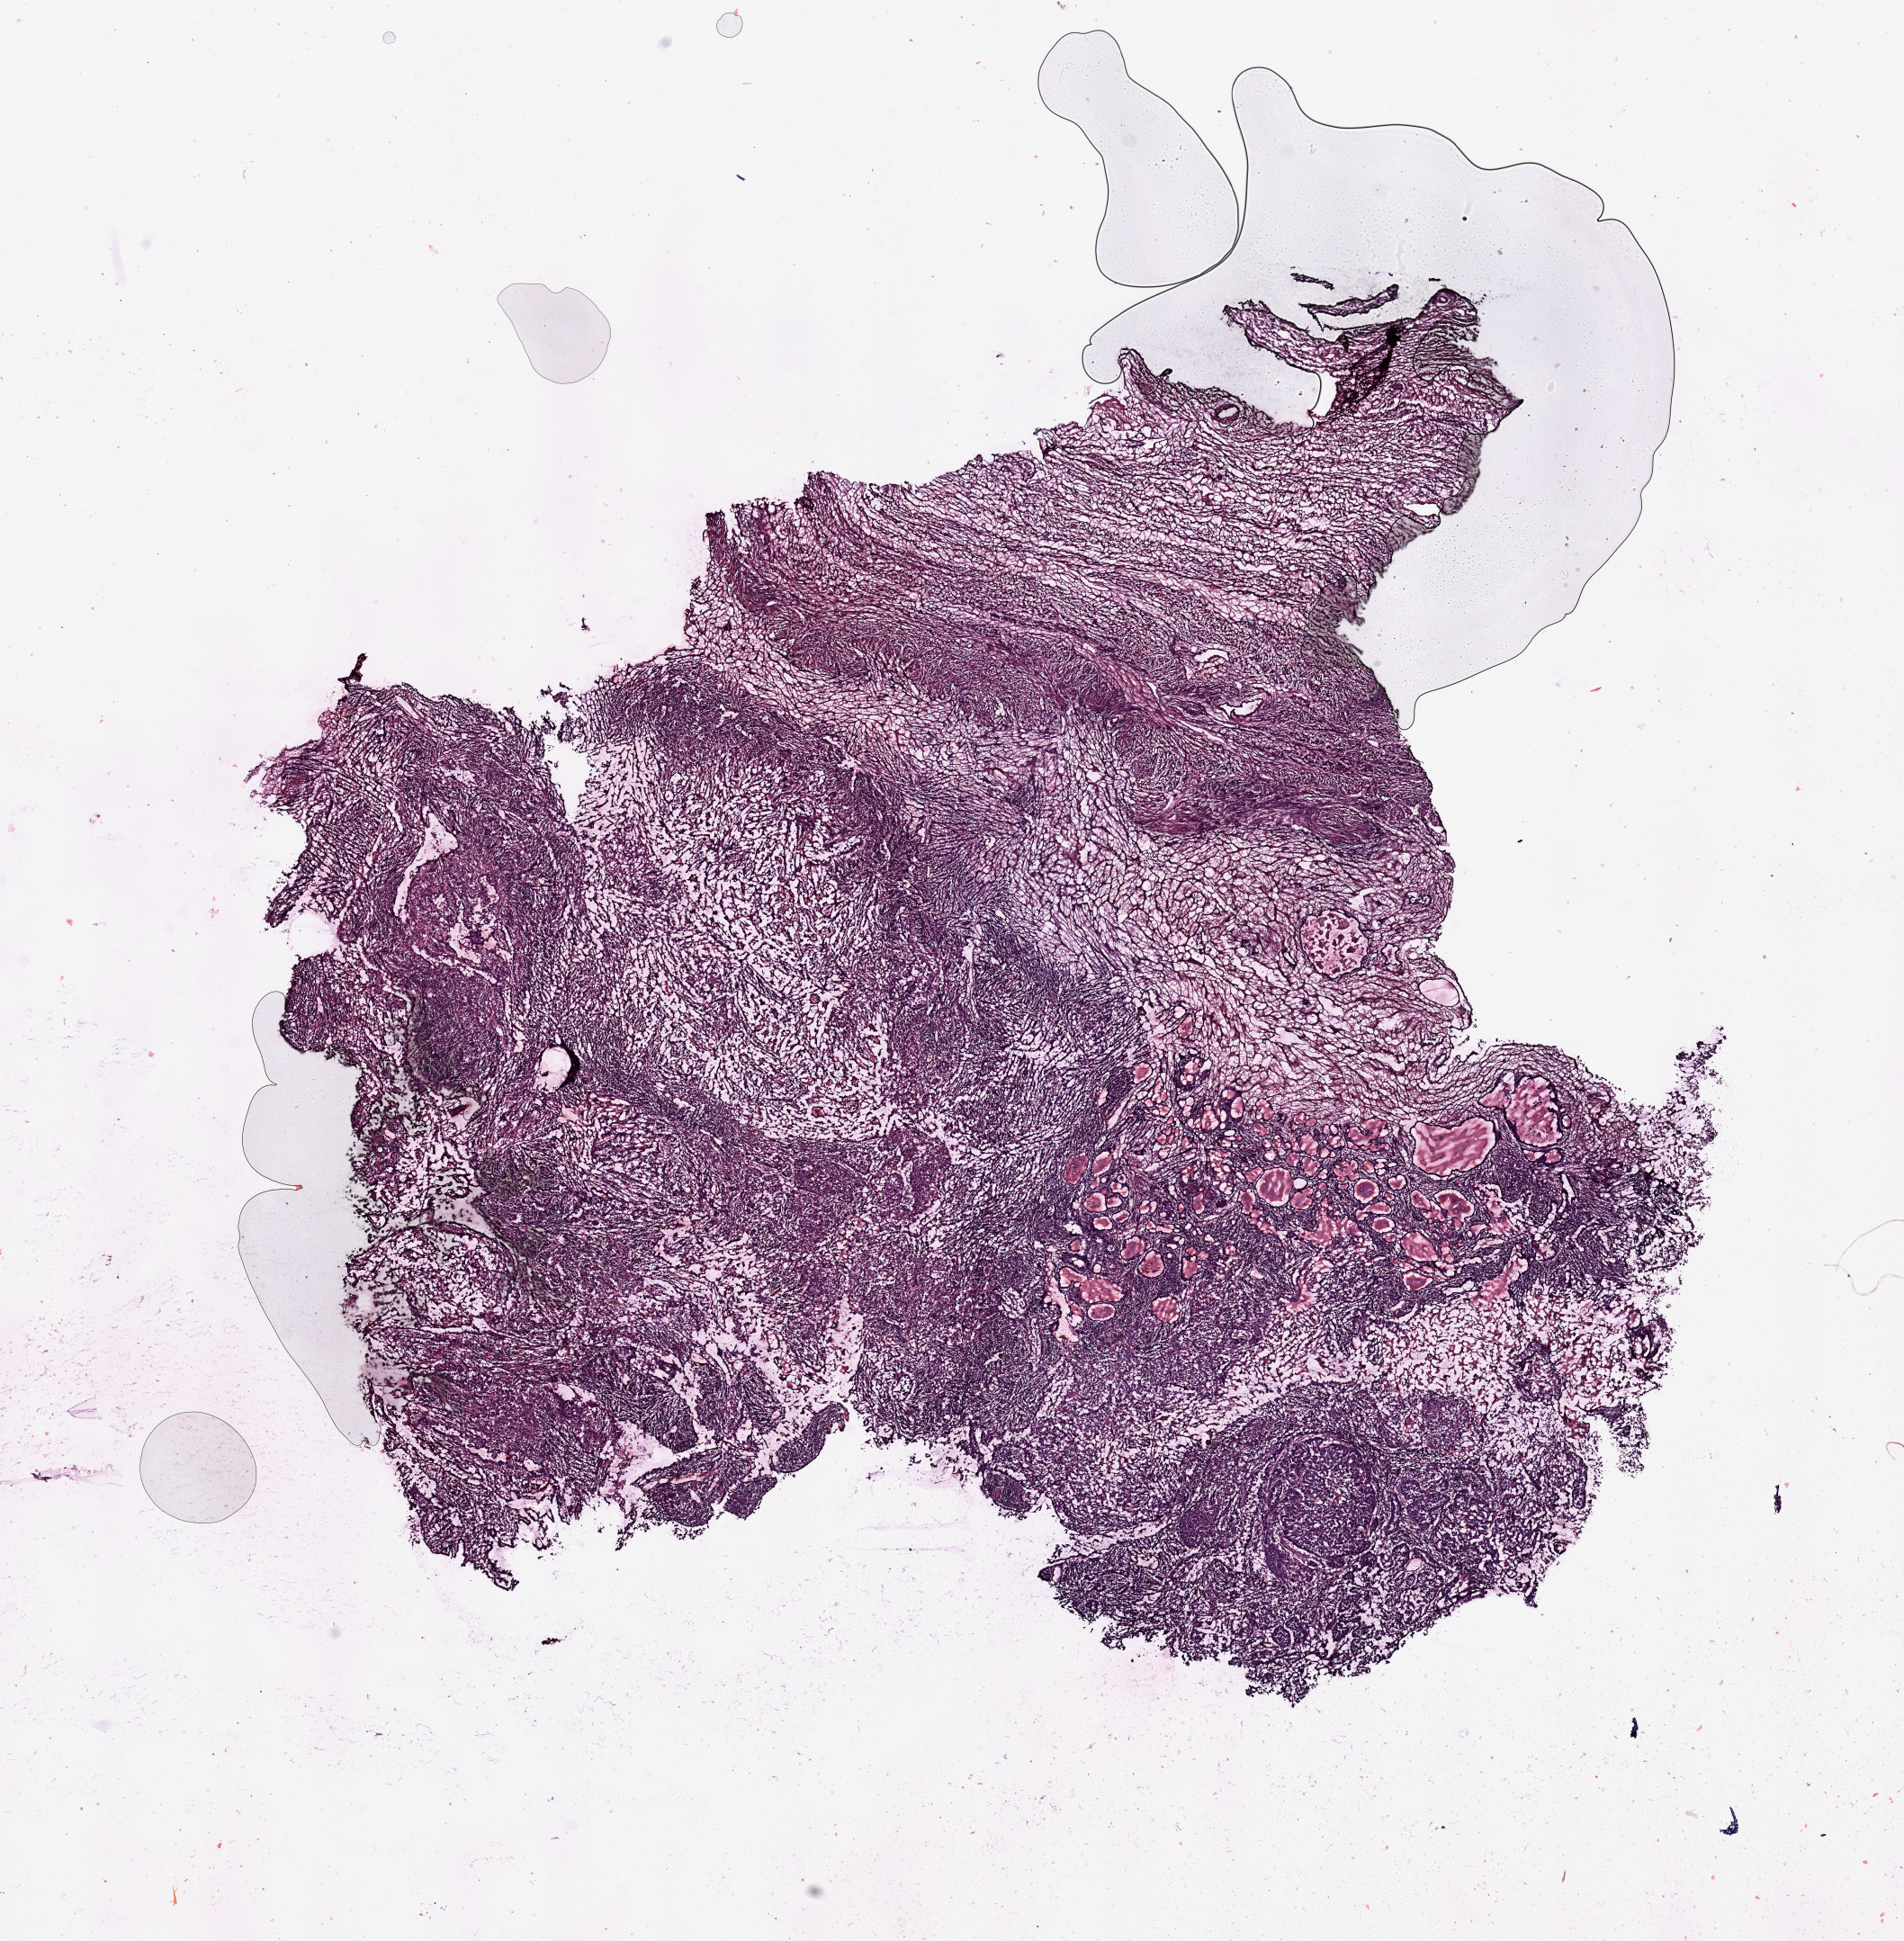
H&E-stained whole-slide image — whole scanned area (about 16.7 x 17.1 mm, from a 20x scan) shown as a low-resolution overview; tumour tissue sample, sampled site: uterus. Female, 75 y/o. Histologic grade: G3 (poorly differentiated). Composition of this section per pathologist review: tumour nuclei 80%, necrosis 0%.
Diagnosis: Endometrioid adenocarcinoma, NOS. AJCC pathologic stage: I.